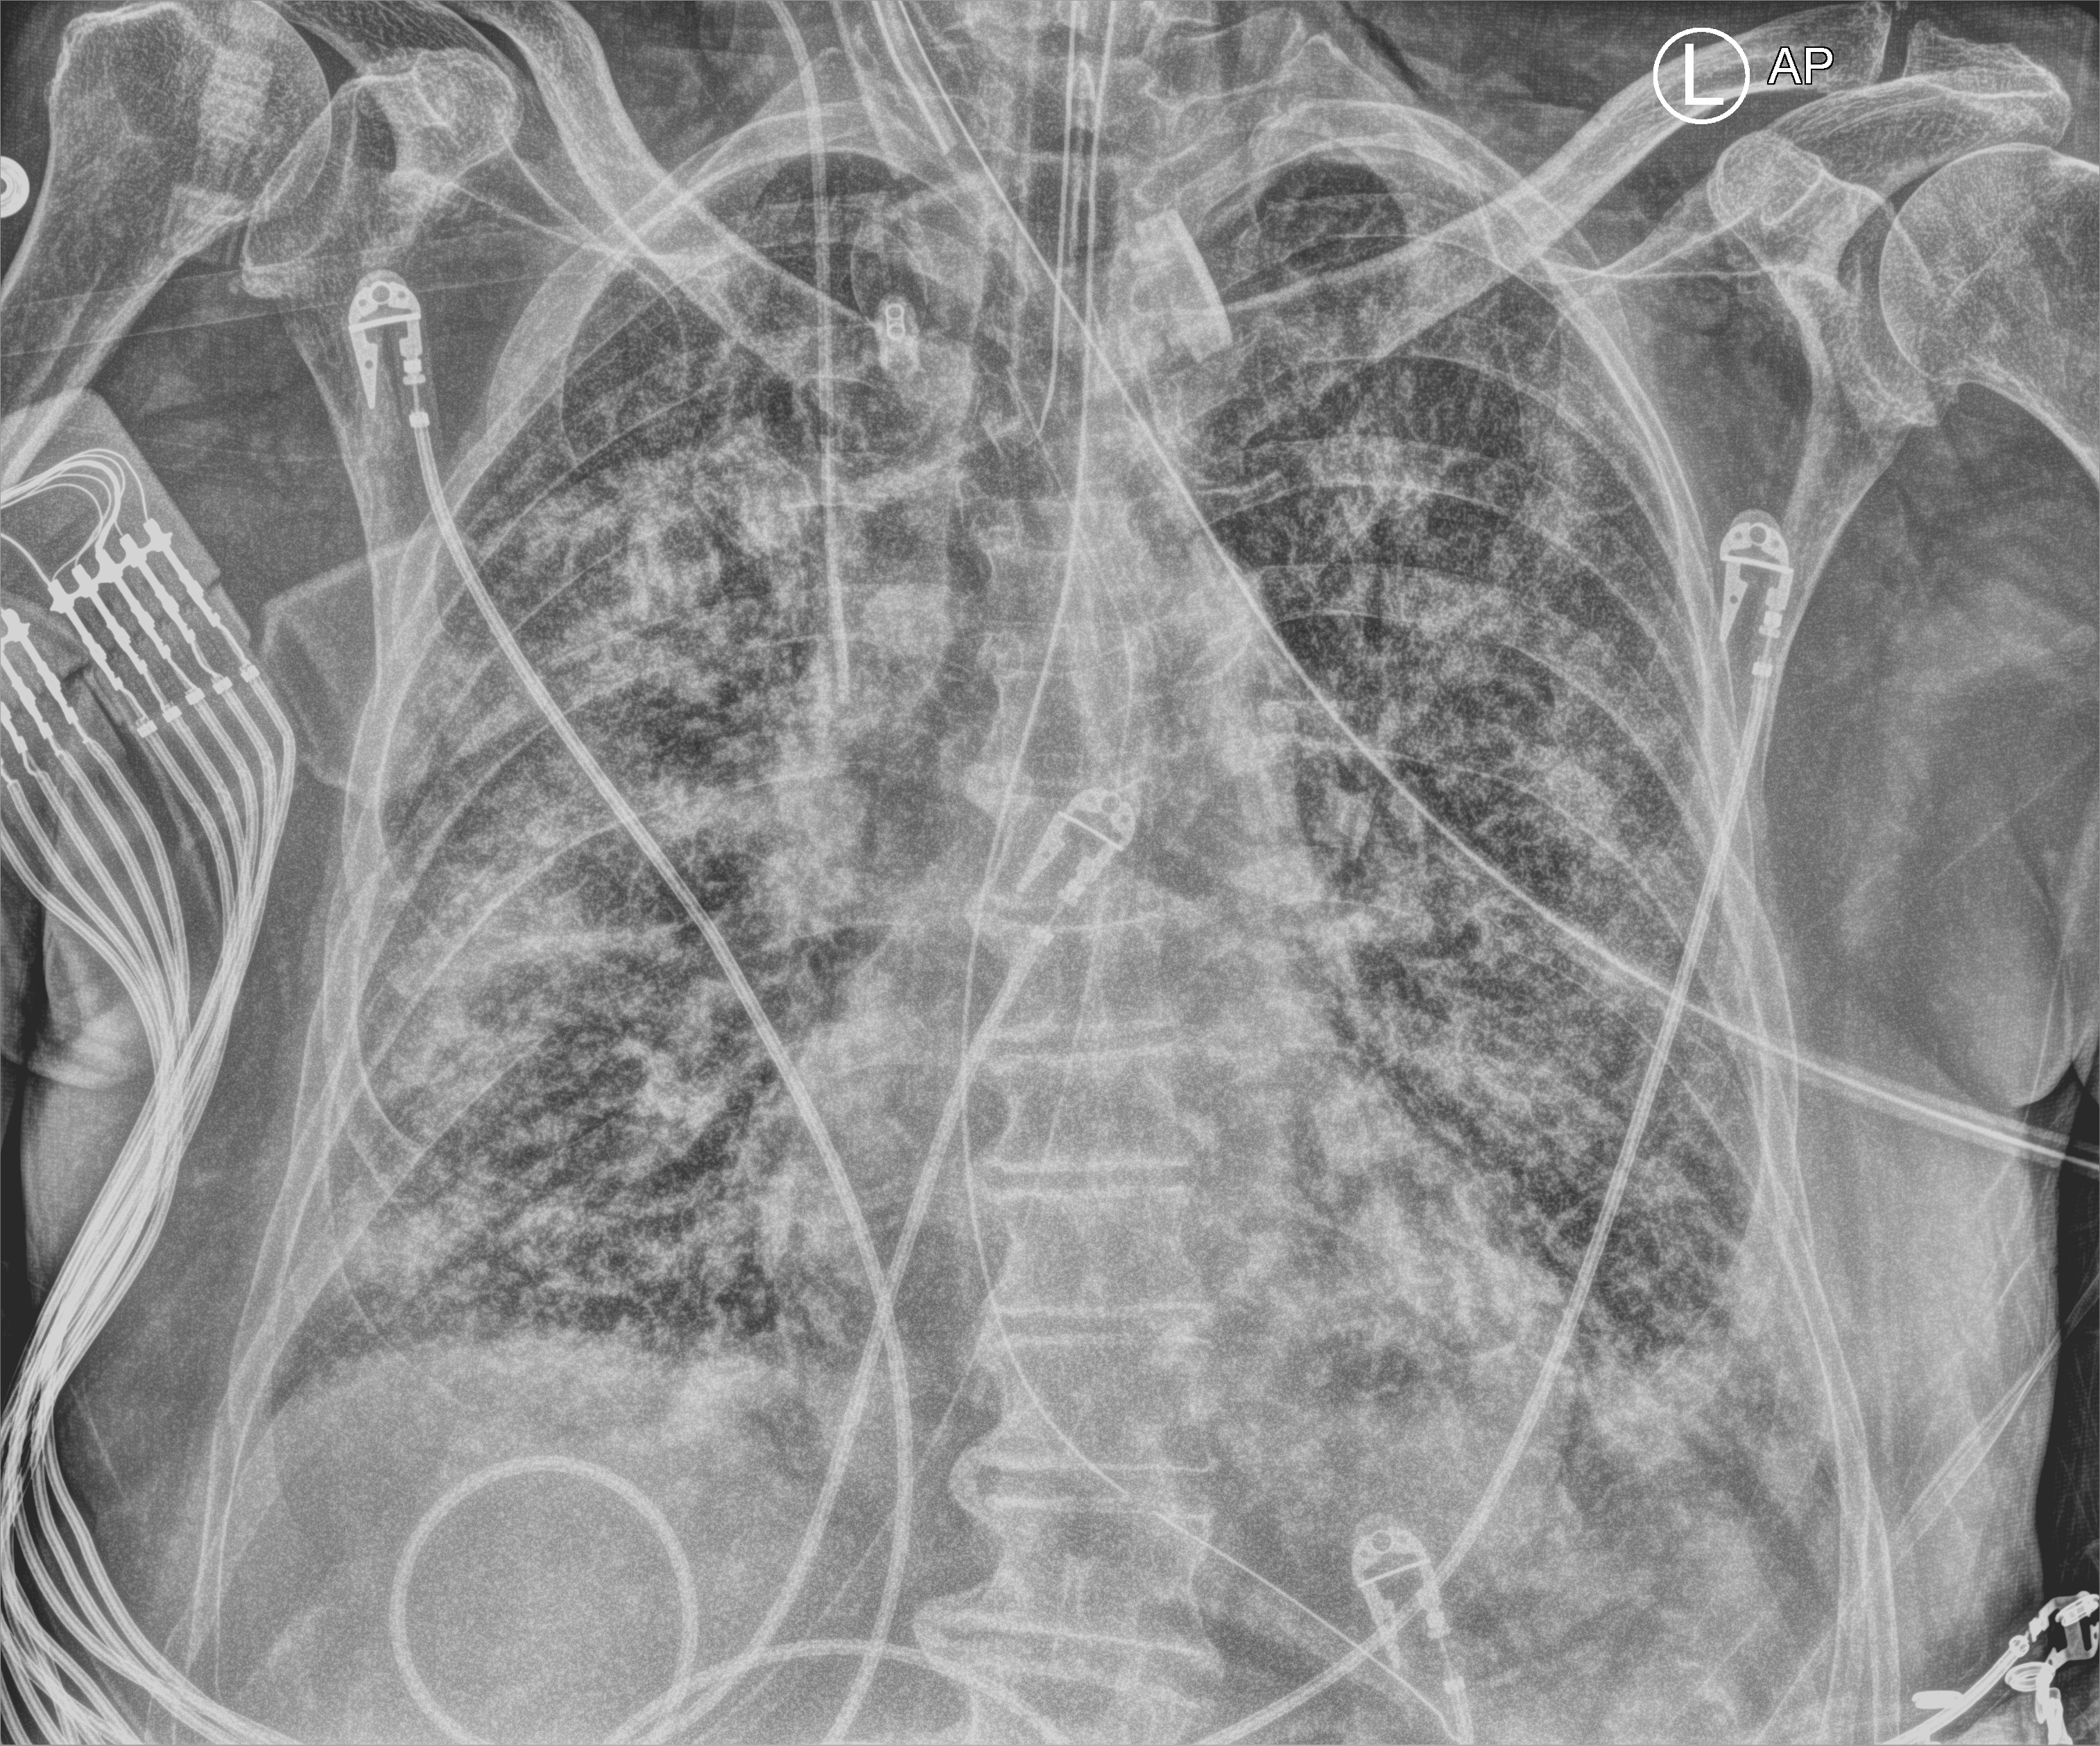
Bedside chest radiograph (computed radiography); anteroposterior (AP) projection. Patient hospitalised with COVID-19; male, aged 75–90 years.
Hospital-stay facts (about this admission, not read from this image; timing relative to this image not recorded): mechanically ventilated during this hospital stay: yes.